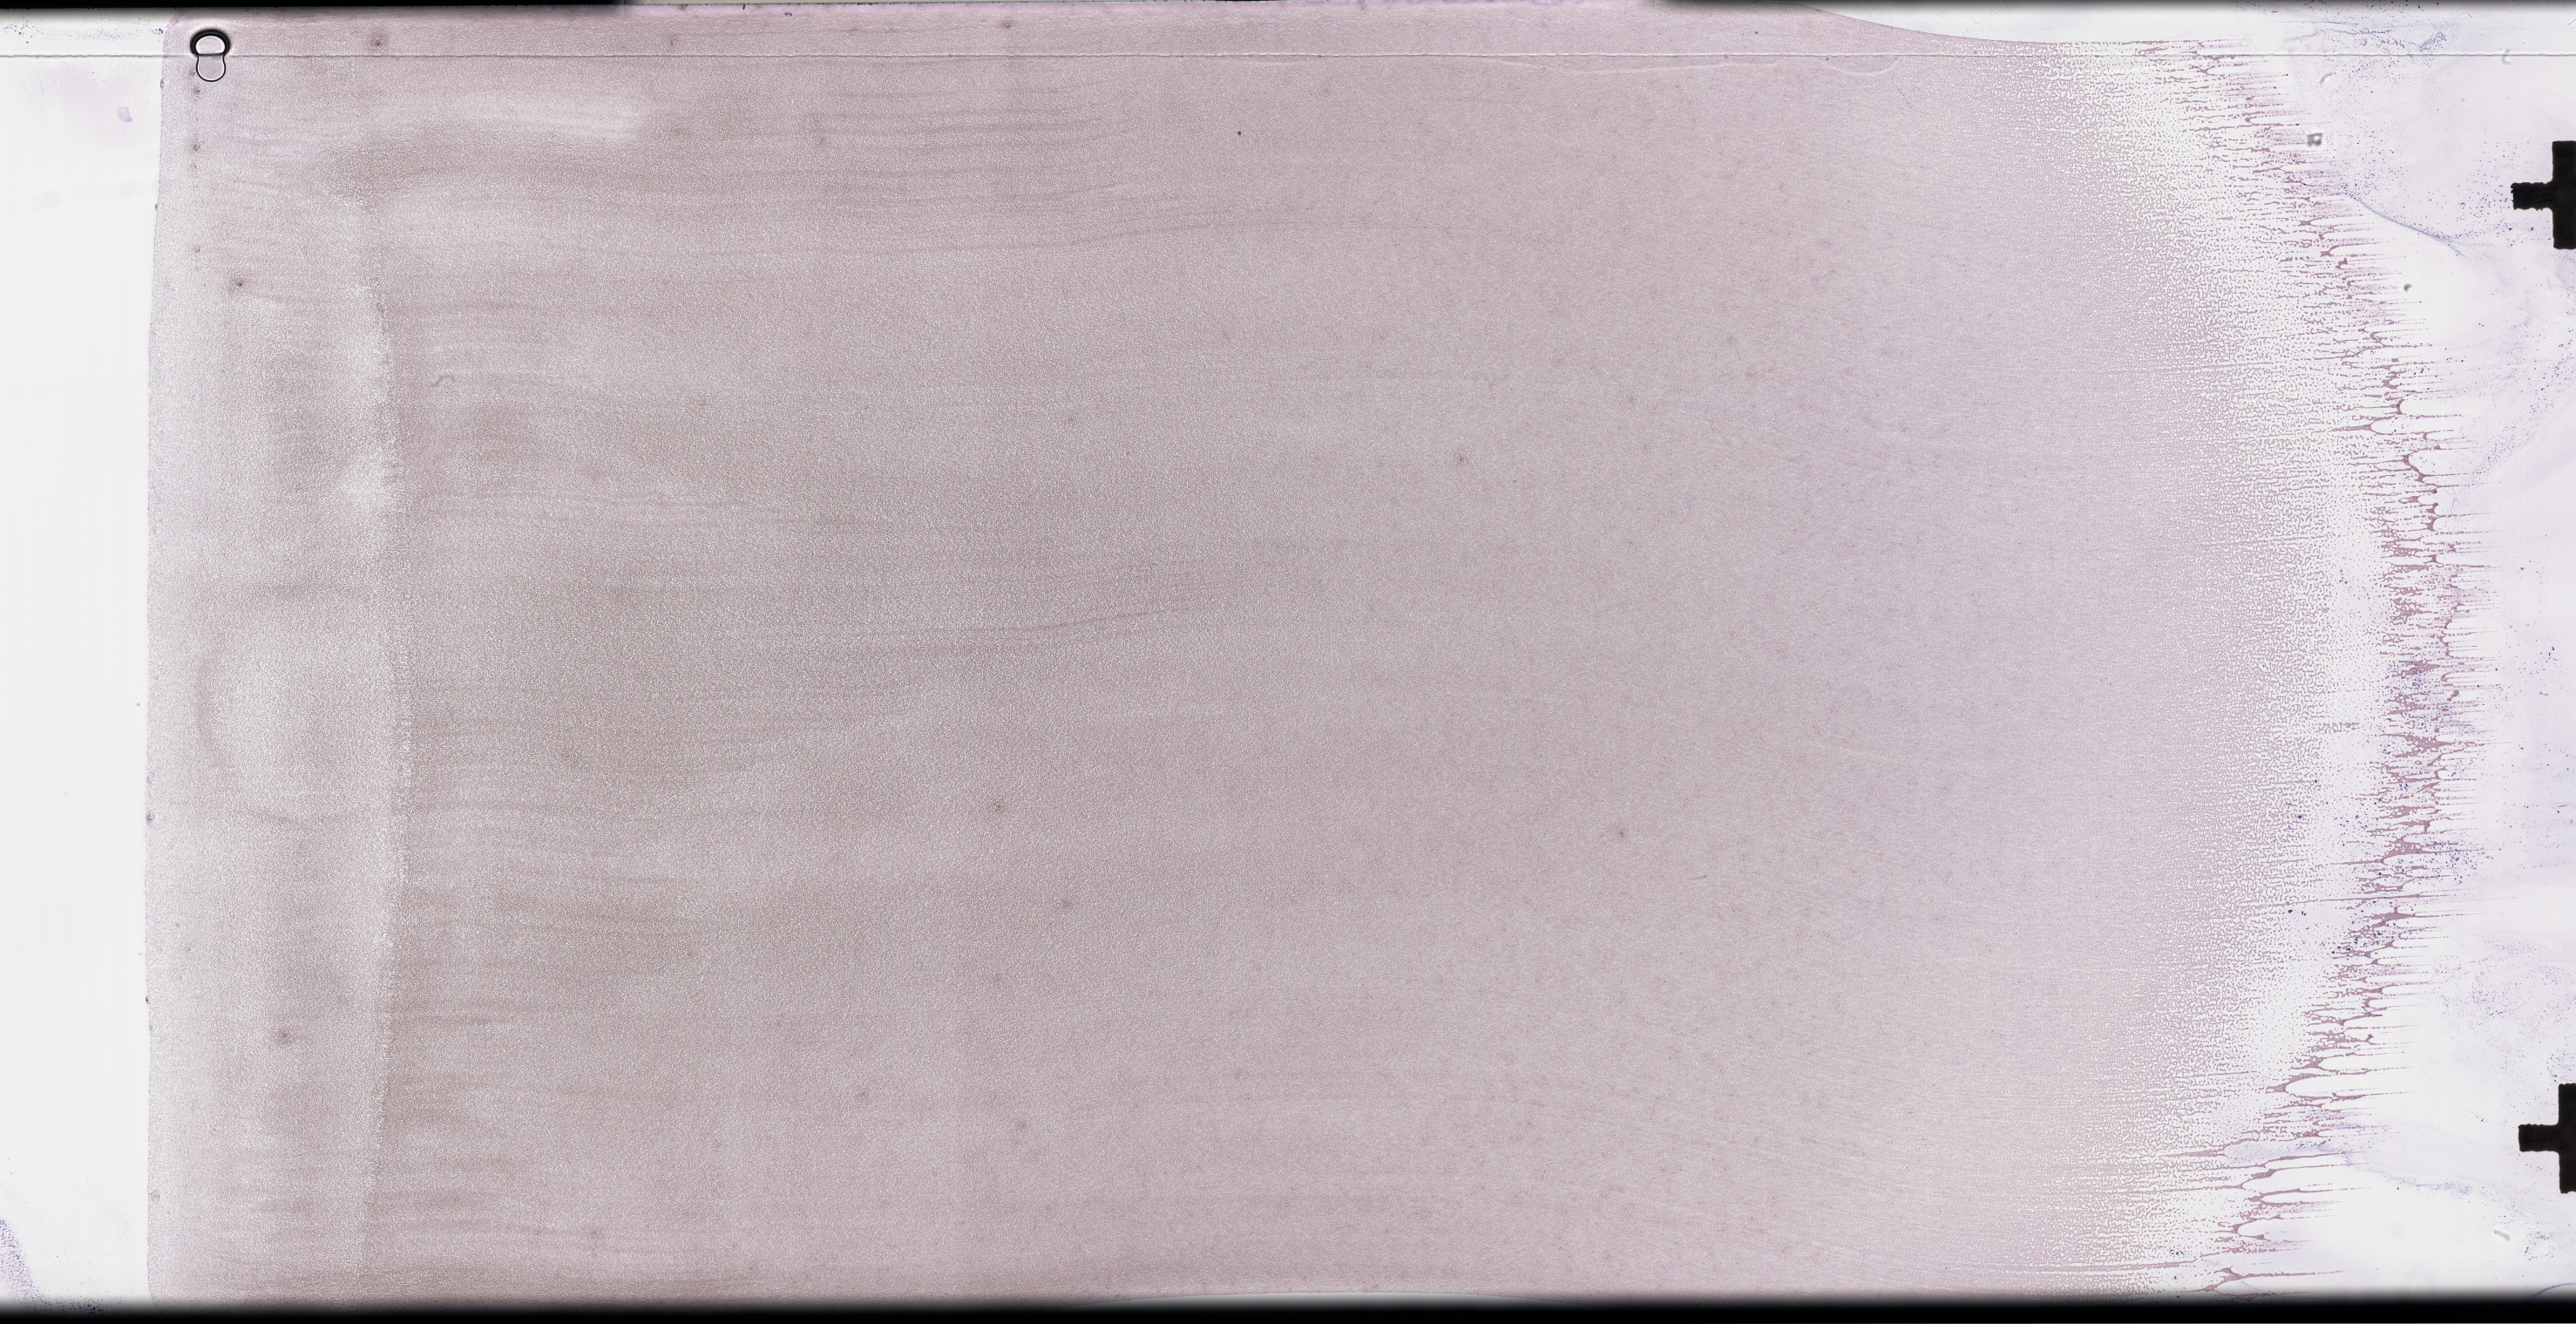
Whole-slide image of a whole blood smear, Wright–Giemsa stain, a low-resolution overview of the entire scanned area, about 47.7 x 24.5 mm. Patient: female.
- from a patient with: Plasma Cell Myeloma